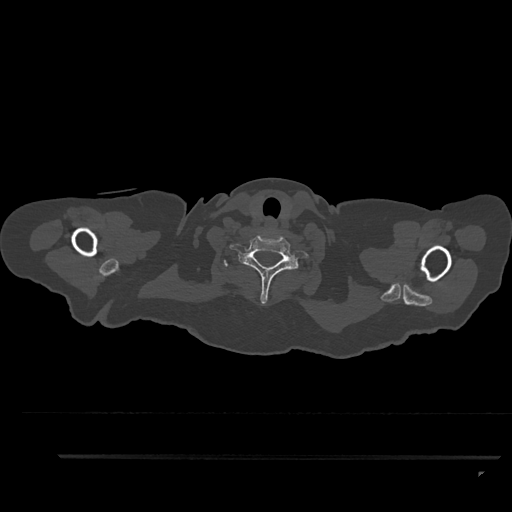
CT including the spine, one axial slice; position 792 of 797 along the scan axis; 120 kVp; bone window (W 1800 / L 400 HU); 0.5 mm slice thickness; 512 × 512 image matrix. Patient: female, 44 years. From the clinical record (not read from this slice): primary cancer: renal.
Outlined on this slice (semi-automatic segmentation, software-assisted and operator-edited):
- T1 vertebra: box from (x=224, y=260) to (x=228, y=267) px